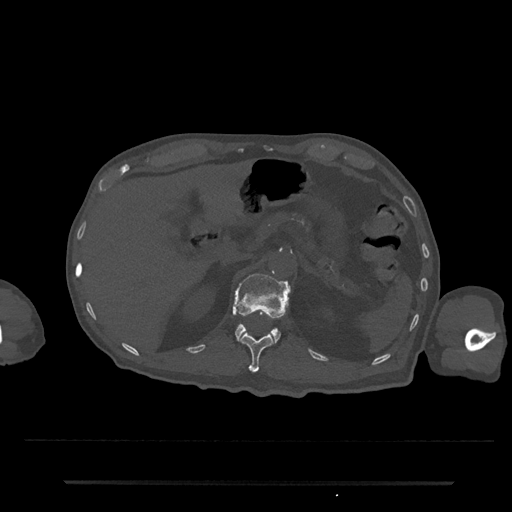
CT including the spine, one axial slice. Slice 168 of 797 in the series (ordered by position). Reconstruction kernel Br40s/3. 120 kVp. Bone window (W 1800 / L 400 HU). 512 × 512 image matrix, field of view 427 × 427 mm. Male patient, age 74 years. Case-level facts recorded for this patient, not image findings: primary cancer: prostate.
Structures marked on this image (semi-automatic segmentation, software-assisted and operator-edited):
- L1 vertebra: bounding box [x1, y1, x2, y2] px = [232, 274, 291, 343]
- T12 vertebra: [240, 333, 274, 372]